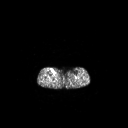
FDG PET of an extremity soft-tissue mass (from a PET/CT study), one axial slice; position 132 of 267 along the scan axis; 3.27 mm slice thickness; 128 × 128 image matrix, field of view 700 × 700 mm. Patient: female, 65 years. From the clinical record (not read from this slice): histological type: undifferentiated – high grade; grade: high; site of the primary tumour: right thigh.
Outlined on this slice (expert contour drawn on MRI and transferred to this co-registered scan by the dataset authors):
- gross tumour volume (mass): bounding box [x1, y1, x2, y2] px = [51, 69, 55, 74]